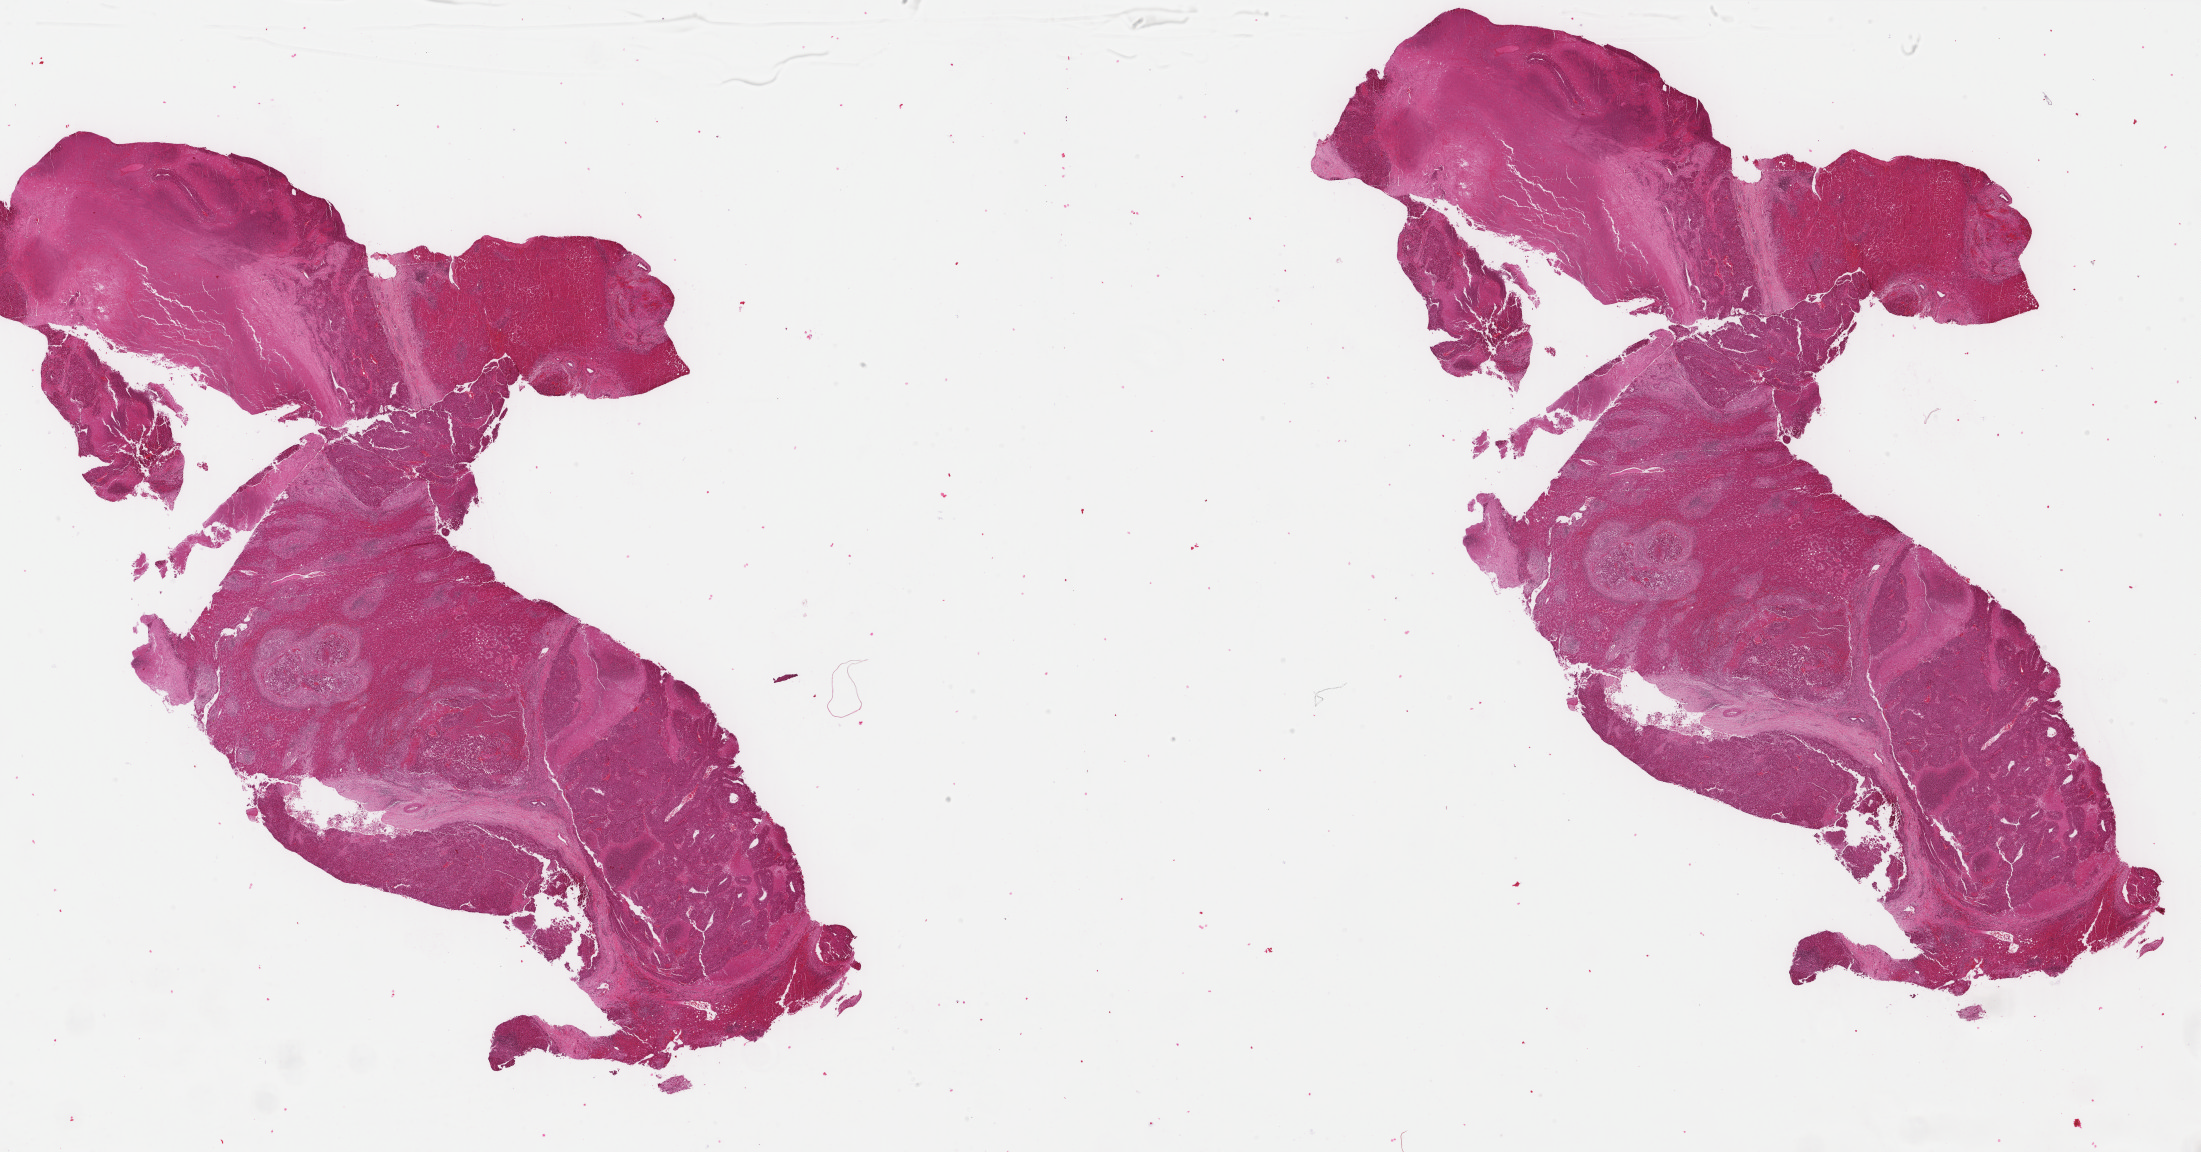
Whole-slide histology image, Hematoxylin and eosin (H&E) stained — a low-resolution overview of the entire scanned area, about 34.9 x 18.3 mm; formalin-fixed paraffin-embedded (FFPE) diagnostic section; primary tumour sample from the liver. Patient: male, age at initial diagnosis 73 years. Histologic grade: G3 (poorly differentiated).
* AJCC pathologic stage: IIIA (6th edition)
* pathologic diagnosis: Hepatocellular carcinoma, NOS